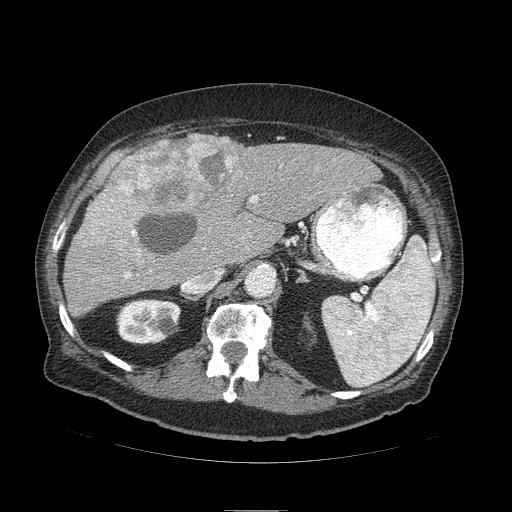
Contrast-enhanced abdominal CT (liver protocol), one axial slice. Position 58 of 103 along the scan axis. Reconstruction kernel STANDARD. Soft-tissue window (W 400 / L 40 HU). 512 × 512 image matrix, field of view 440 × 440 mm. From the clinical record (not read from this slice): diagnosis: hepatocellular carcinoma (patient treated with transarterial chemoembolisation; whether this scan precedes or follows treatment is not stated here); TNM stage (as recorded): Stage-IIIA; Child-Pugh class: B; tumour differentiation: well differentiated; tumour nodularity: multinodular.
Outlined on this slice (semi-automatically segmented with operator editing):
- liver parenchyma outside the tumour (the mass and vessels are separate outlines, so this box may not span the whole liver): bounding box (x1, y1, x2, y2) in pixels: (62, 136, 381, 316)
- mass: (75, 133, 246, 252)
- liver vessels: (125, 195, 258, 278)